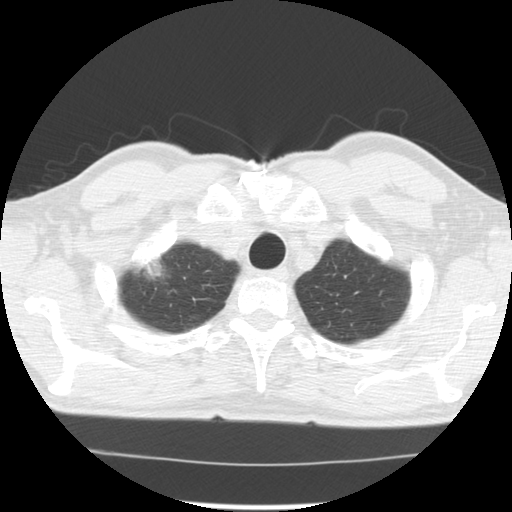
Chest CT (low-dose screening protocol), one axial image. Third screening round (two years after baseline). Lung window (W 1500 / L -600 HU). 2.5 mm slice thickness. Standard (soft-tissue) reconstruction kernel (STANDARD). 512 × 512 image matrix, field of view 340 × 340 mm. Male, age 64 years at enrolment. Former smoker at enrolment.
Lesion marked by an expert reader, bounding box <117,239,185,297> (left, top, right, bottom; pixels). The screening reader recorded 3 non-calcified nodules or masses ≥4 mm on this exam (right upper lobe, right lower lobe, left upper lobe); which of them this box marks is not recorded. Later outcome: lung cancer diagnosed 30 days after this screen — adenocarcinoma, NOS, right upper lobe, well differentiated (G1), stage IB (AJCC 6th edition), 45 mm at pathology.